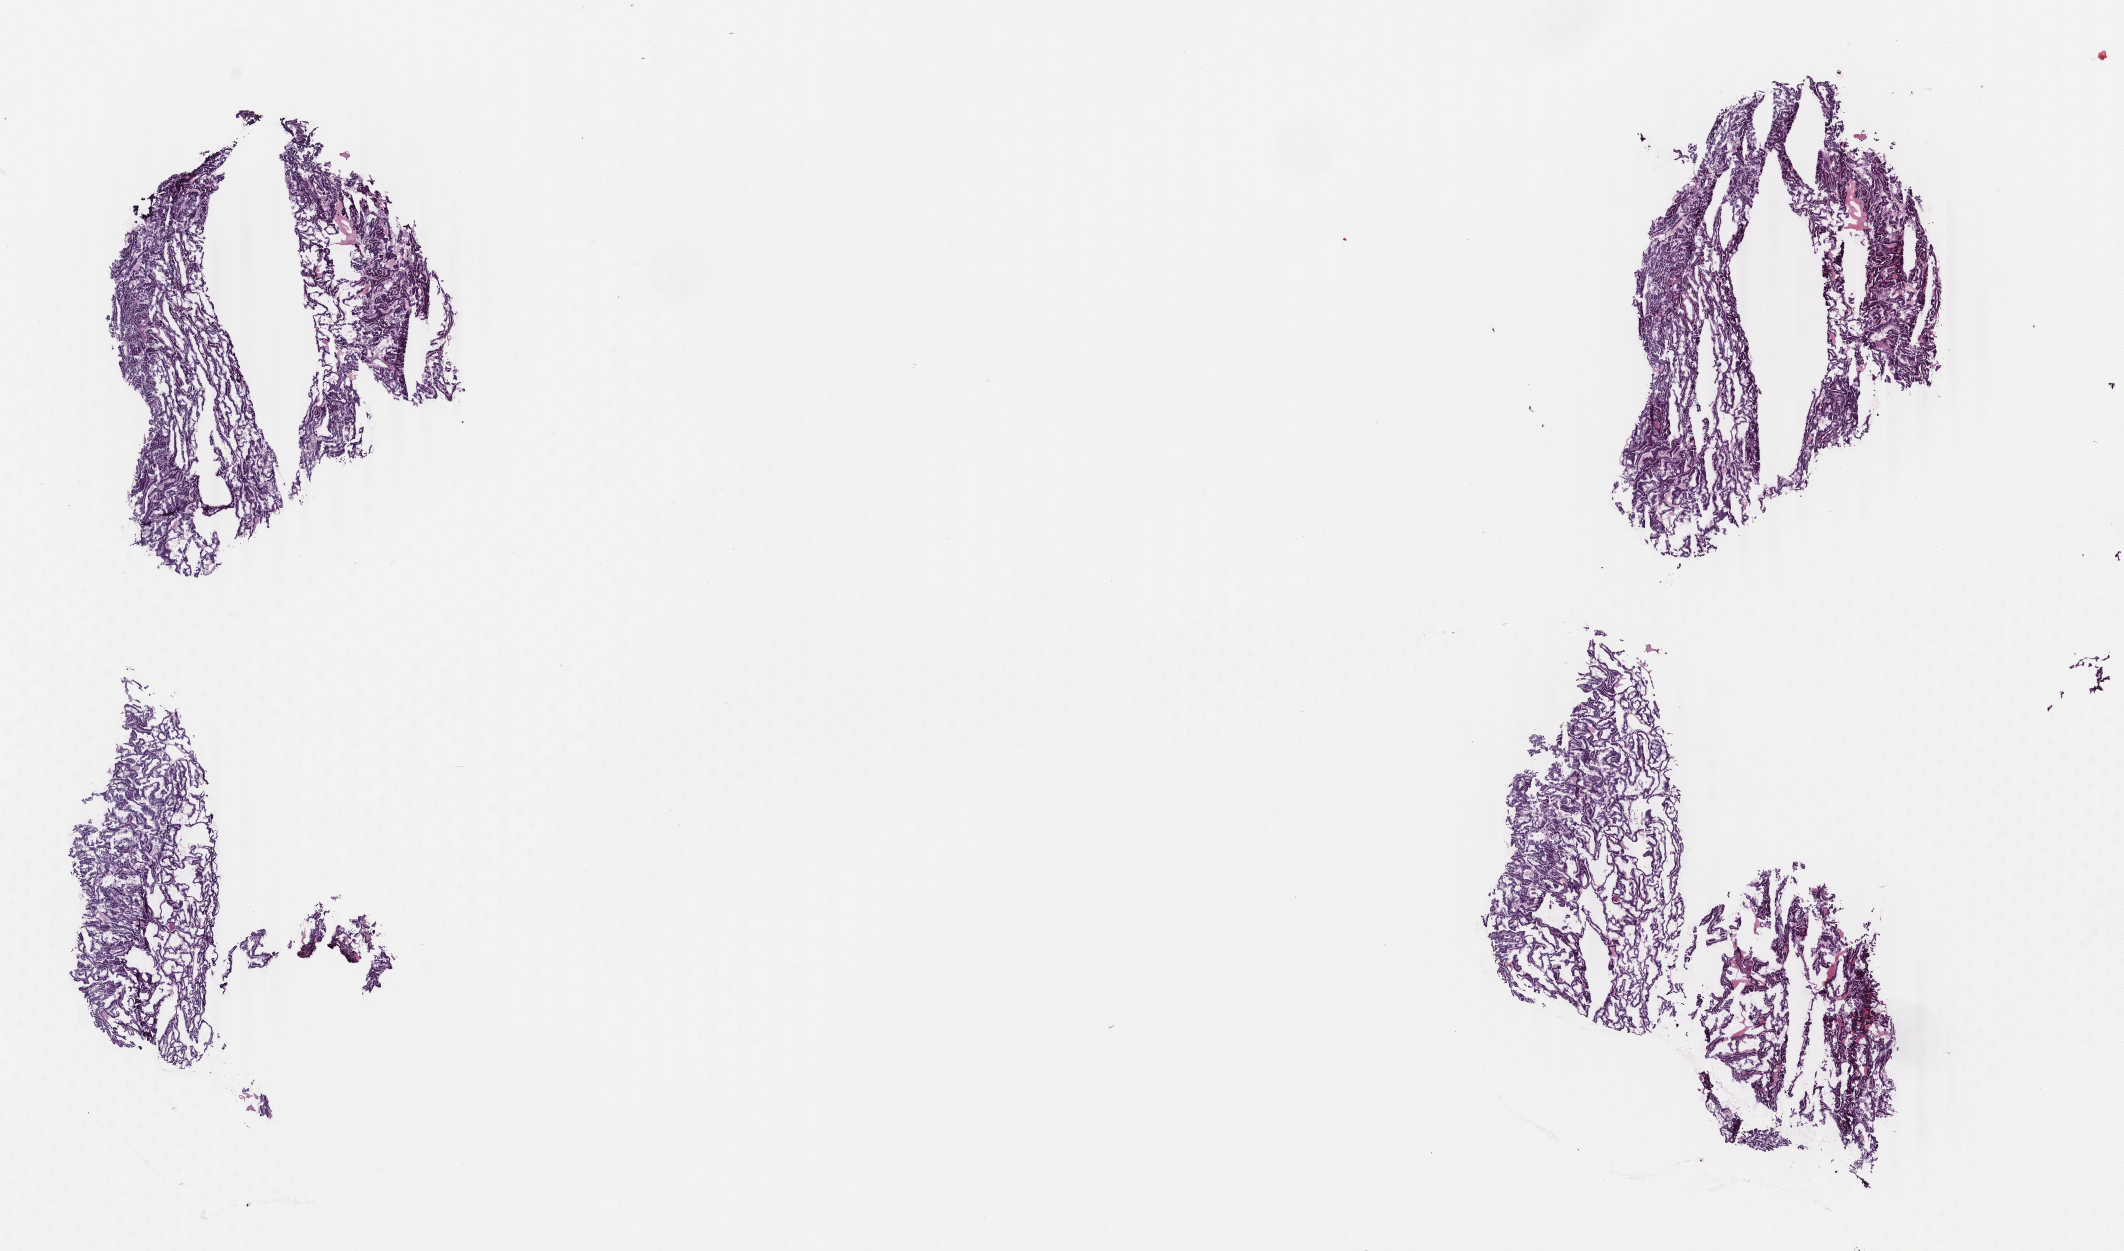
H&E whole-slide image — low-resolution overview of the scanned area, about 16.9 x 10.0 mm, frozen section from the top of the tissue portion, thyroid, primary tumour sample. Patient: female, age at initial diagnosis 41 years. Pathologist review of this section (percent, as recorded): tumour cells 95%, tumour nuclei 100%, normal cells 0%, stromal cells 5%, necrosis 0%. Inflammatory infiltration, as recorded: lymphocyte infiltration 3%, monocyte infiltration 2%, neutrophil infiltration 0%.
TNM: T2 N1 M0. AJCC pathologic stage: I (6th edition). Histologic diagnosis: Papillary adenocarcinoma, NOS.